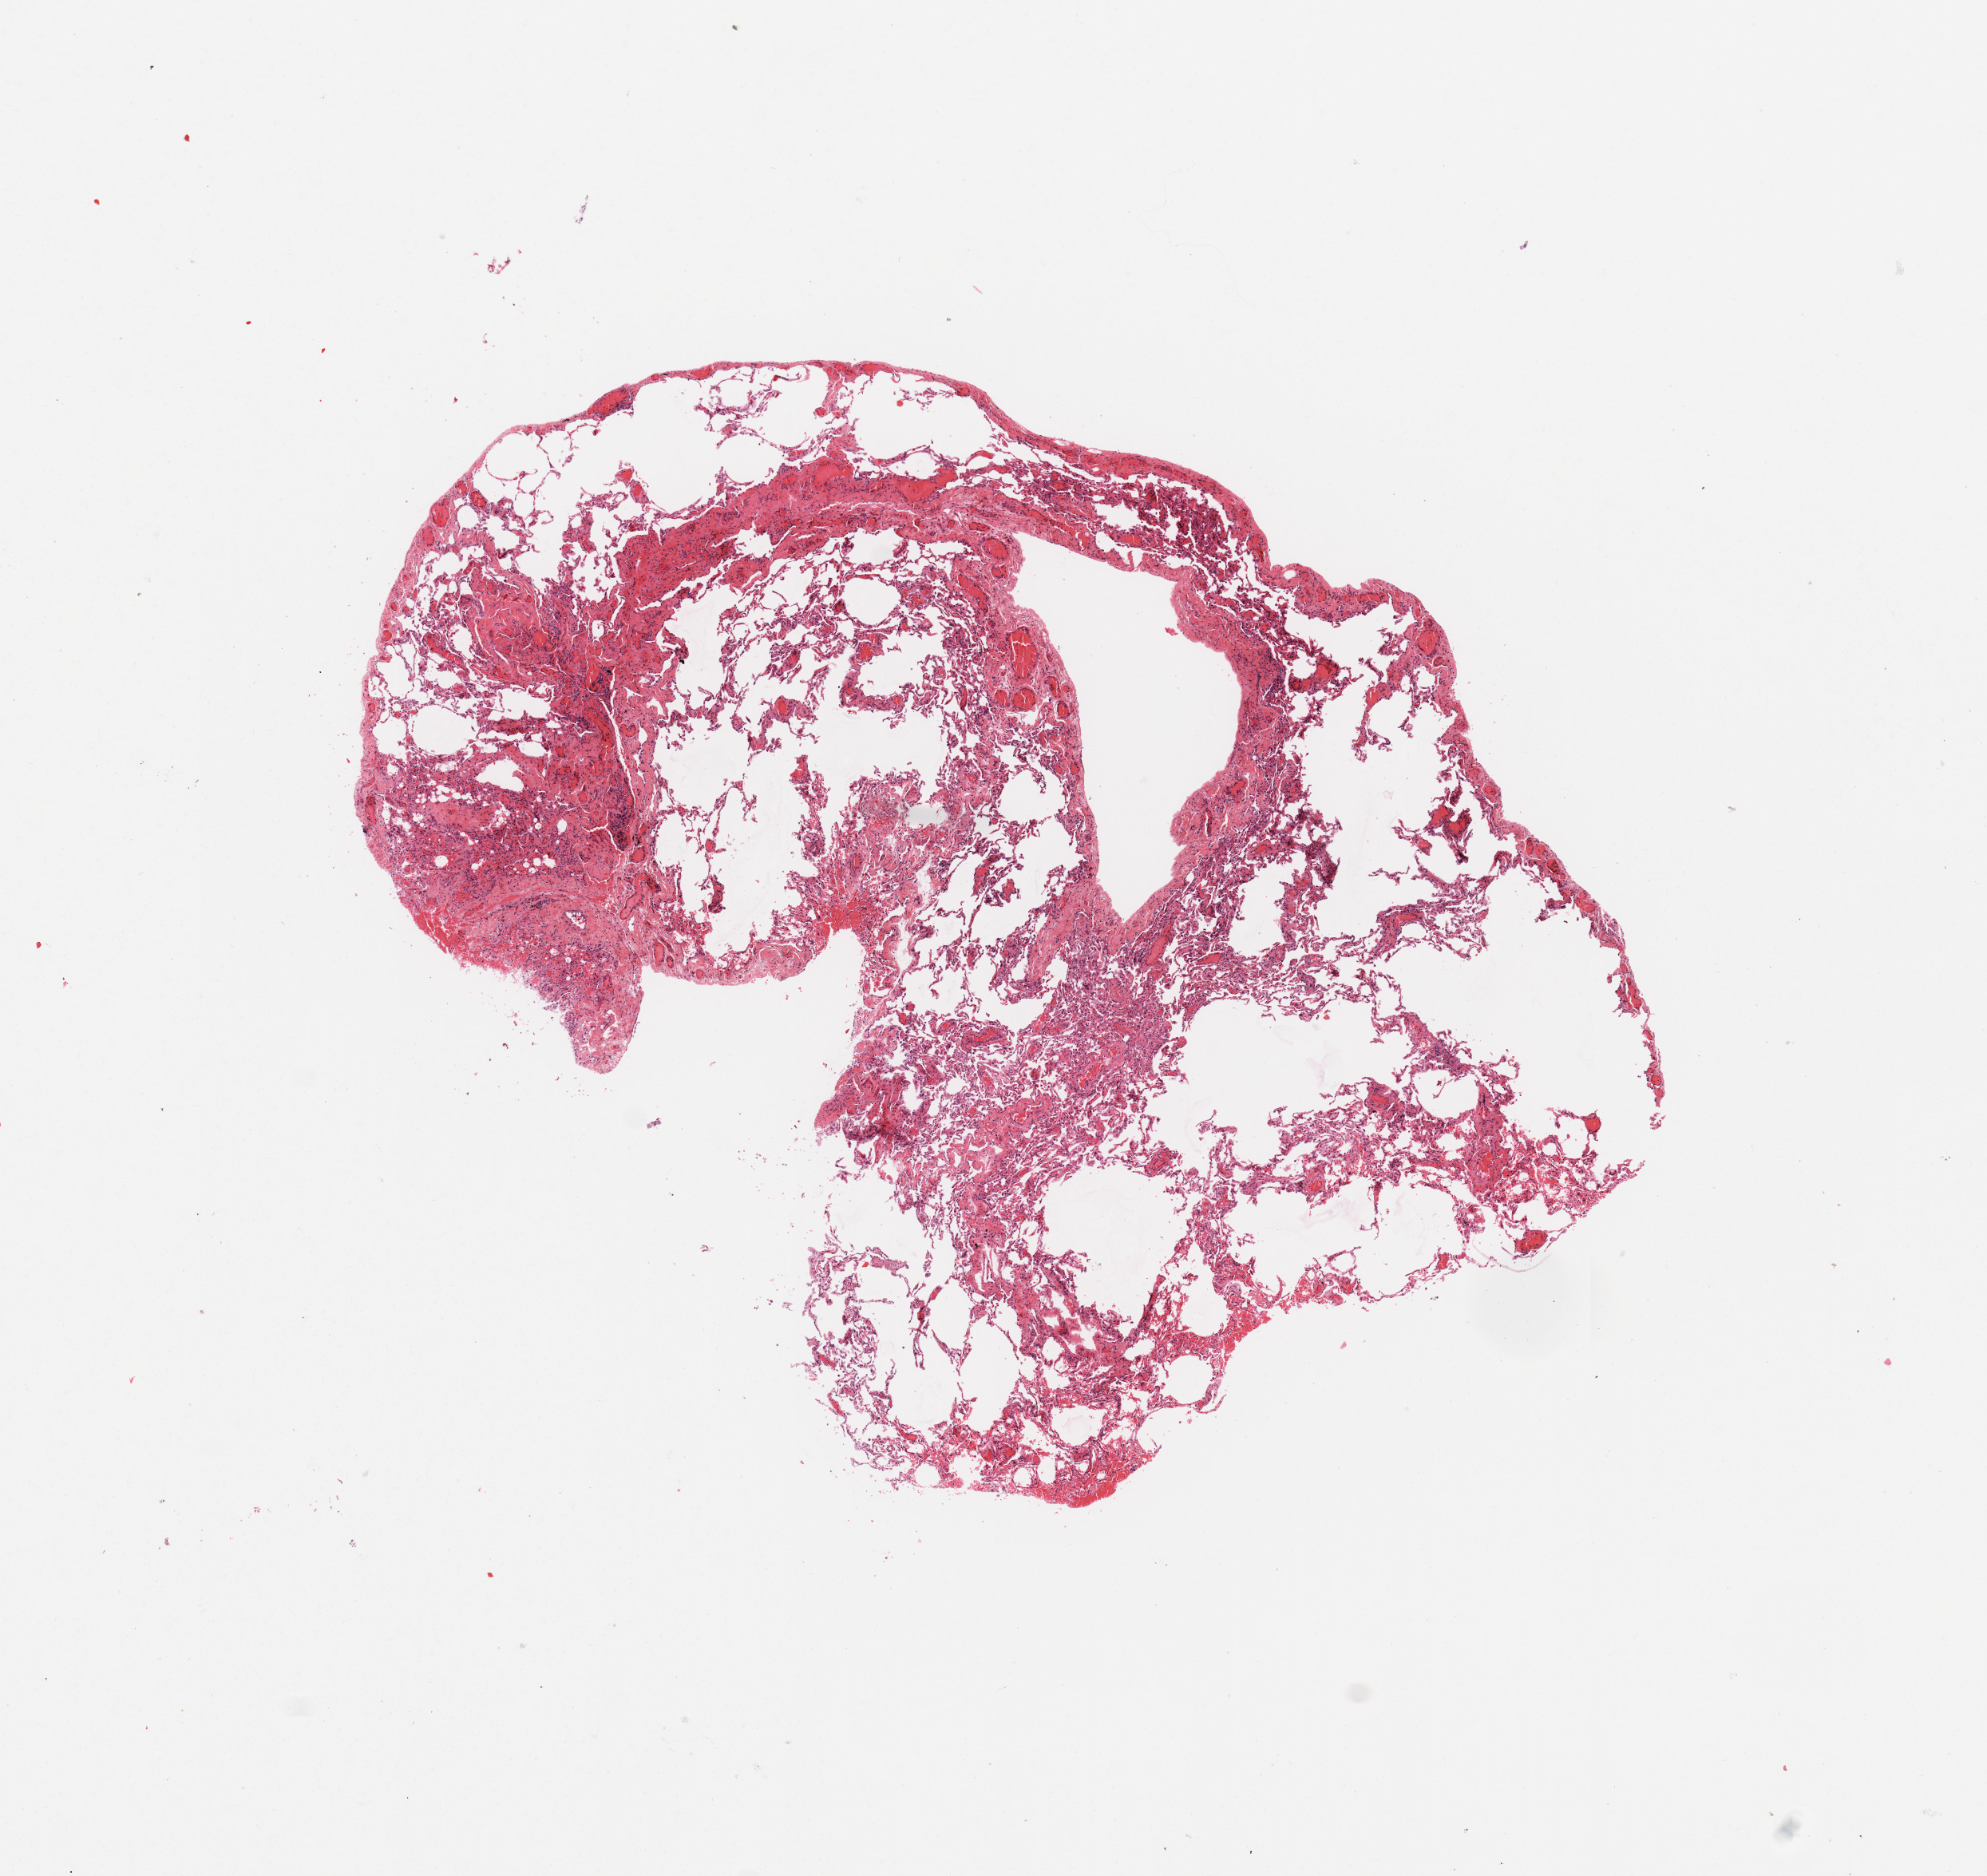
Whole-slide histology image, H&E-stained, shown as a low-resolution overview of the whole scanned area (about 9.8 x 9.3 mm, from a 20x scan). Lung, normal (non-tumour) tissue. Patient: male, age 61 years.
- this section: normal (non-tumour) tissue from the same patient
- patient diagnosis: Adenocarcinoma, NOS